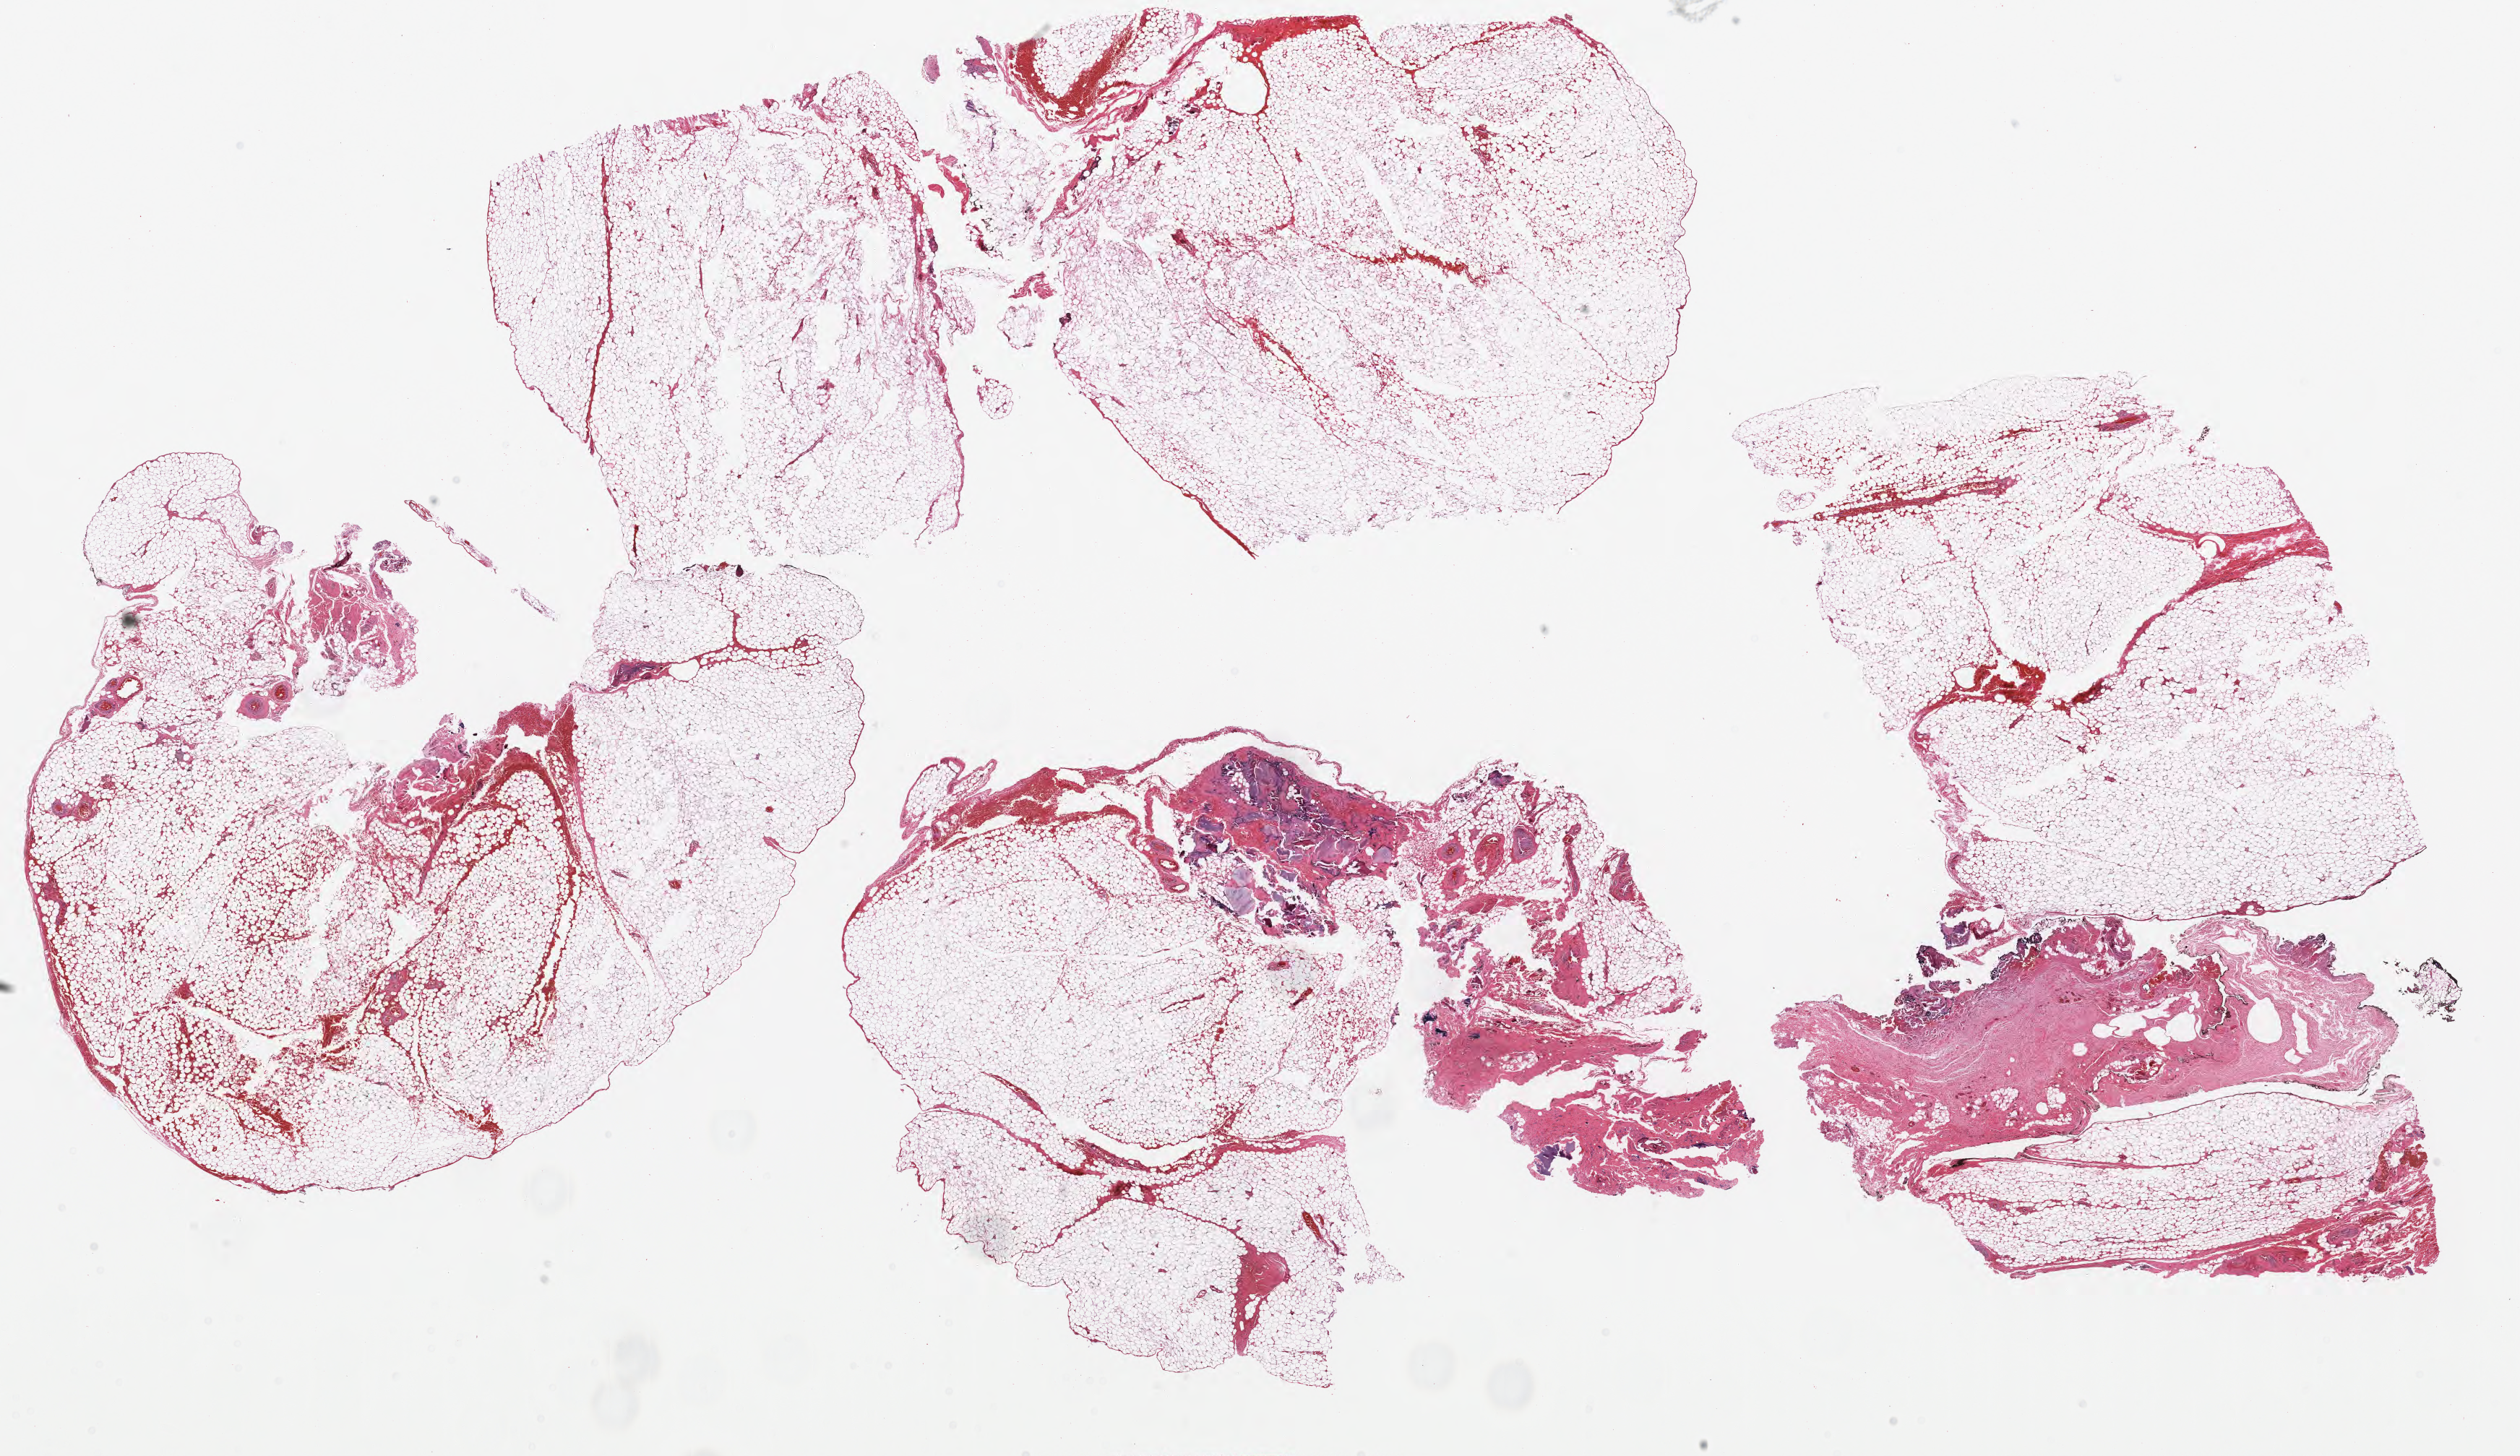
H&E-stained whole-slide image, whole scanned area (about 27.6 x 16.0 mm, from a 40x scan) shown as a low-resolution overview, formalin-fixed paraffin-embedded (FFPE) diagnostic section, primary tumour sample from the thymus. Female patient; age at initial diagnosis 57 years.
Histologic diagnosis: Thymoma, type B1, NOS.